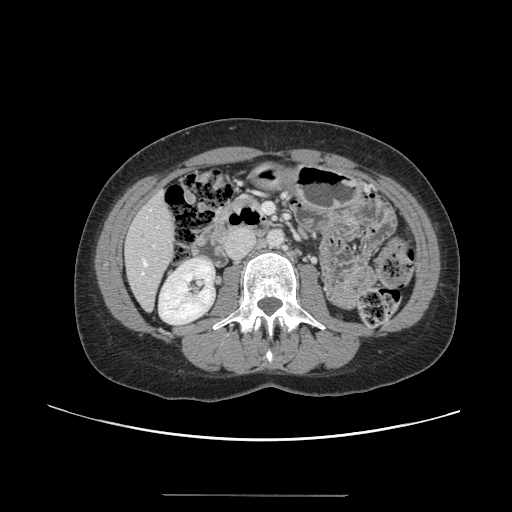
Contrast-enhanced abdominal CT, one axial slice; position 42 of 144 along the scan axis; 120 kVp; intravenous contrast given; soft-tissue window (W 400 / L 40 HU); 2.5 mm slice thickness; 512 × 512 image matrix. Female patient, age 53 years. Case-level facts recorded for this patient, not image findings: diagnosis: colorectal cancer liver metastases, imaged before liver resection; multiple liver metastases: yes; largest metastasis: 1.1 cm; disease in both lobes: no.
Outlined on this slice (manually delineated by an expert):
- hepatic veins: bounding box <142,260,147,274> (left, top, right, bottom; pixels)
- liver: <125,195,176,309>
- planned liver remnant (the part of the liver to remain after resection): <126,194,176,308>
- portal vein (with intrahepatic branches): <153,245,155,247>